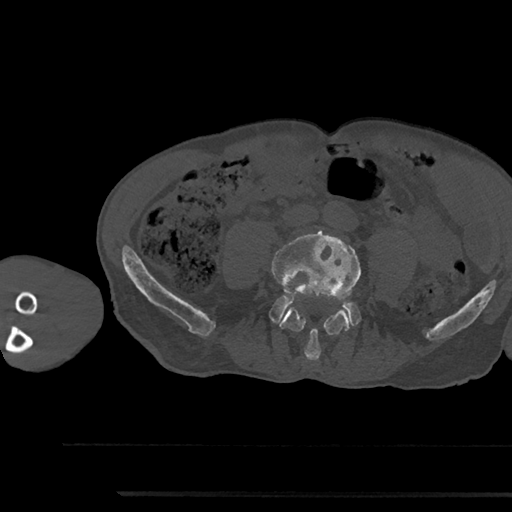
CT including the spine, one axial slice; position 388 of 797 along the scan axis; reconstruction kernel Br40s/3; 120 kVp; bone window (W 1800 / L 400 HU); 512 × 512 image matrix, field of view 367 × 367 mm. Patient: male, 79 years. Case-level facts recorded for this patient, not image findings: primary cancer: prostate.
Annotated regions visible in this slice (semi-automatically segmented with operator editing):
- L4 vertebra: box from (x=272, y=231) to (x=361, y=361) px
- L5 vertebra: (x=270, y=296)–(x=360, y=326)